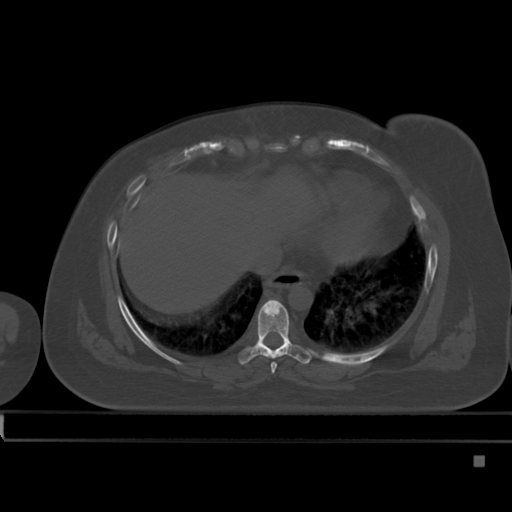
CT including the spine, one axial slice. Slice 278 of 495 in the series (ordered by position). Bone window (W 1800 / L 400 HU). 1.5 mm slice thickness. 512 × 512 image matrix. Female patient, age 33 years. From the clinical record (not read from this slice): primary cancer: breast.
Outlined on this slice (semi-automatic segmentation, software-assisted and operator-edited):
- T7 vertebra: bounding box <271,362,277,373> (left, top, right, bottom; pixels)
- T8 vertebra: <239,299,312,365>